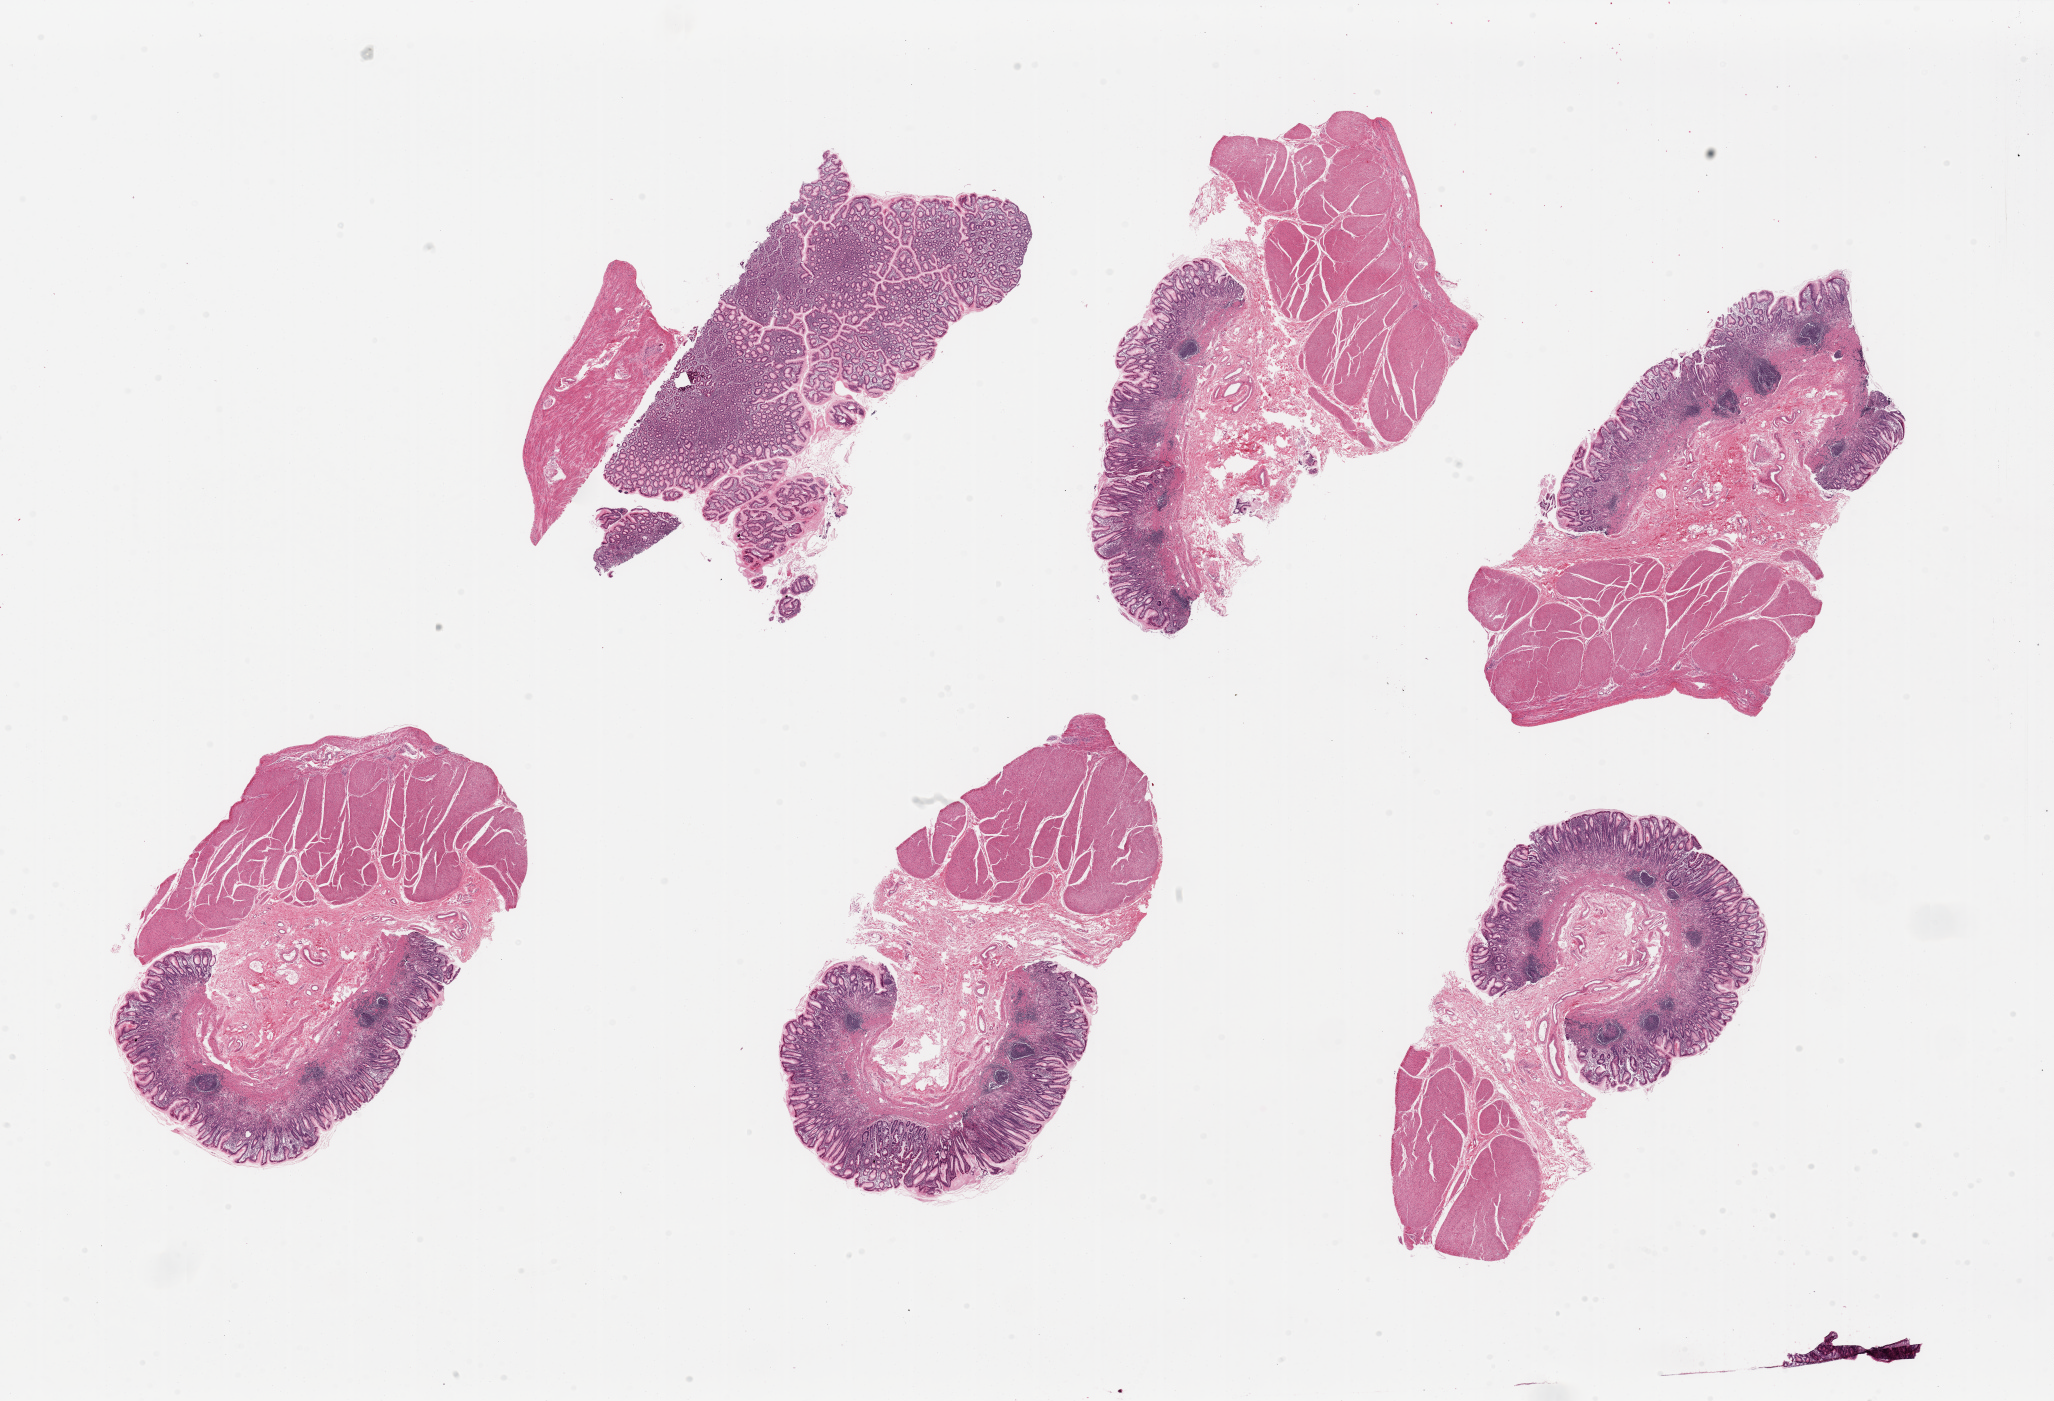
Hematoxylin and eosin (H&E) whole-slide image, low-resolution overview of the scanned area, about 32.5 x 22.2 mm (acquisition: 20x scan). PAXgene-fixed, paraffin-embedded tissue. Sampled site (target tissue): stomach. Donor tissue sample. Donor sex: female.
- reviewer comment on this tissue sample: 6 pieces, up to 8x6mm; well preserved. Marked chronic active gastritis with patchy intestinal metaplasia, gastropathic changes with foveolar hyperplasia, features suggest possible H pylori infection